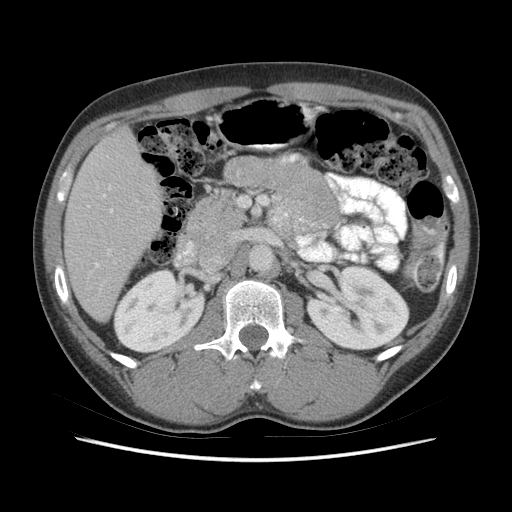
Contrast-enhanced abdominal CT (liver protocol), one axial slice. Position 24 of 73 along the scan axis. 140 kVp. Soft-tissue window (W 400 / L 40 HU). 2.5 mm slice thickness. 512 × 512 image matrix, field of view 360 × 360 mm. From the clinical record (not read from this slice): diagnosis: hepatocellular carcinoma (patient treated with transarterial chemoembolisation; whether this scan precedes or follows treatment is not stated here); TNM stage (as recorded): Stage-IIIA; Child-Pugh class: A; tumour nodularity: multinodular.
Annotated regions visible in this slice (semi-automatically segmented with operator editing):
- liver parenchyma outside the tumour (the mass and vessels are separate outlines, so this box may not span the whole liver): bounding box (x1, y1, x2, y2) in pixels: (64, 128, 162, 320)
- liver vessels: (88, 187, 113, 268)